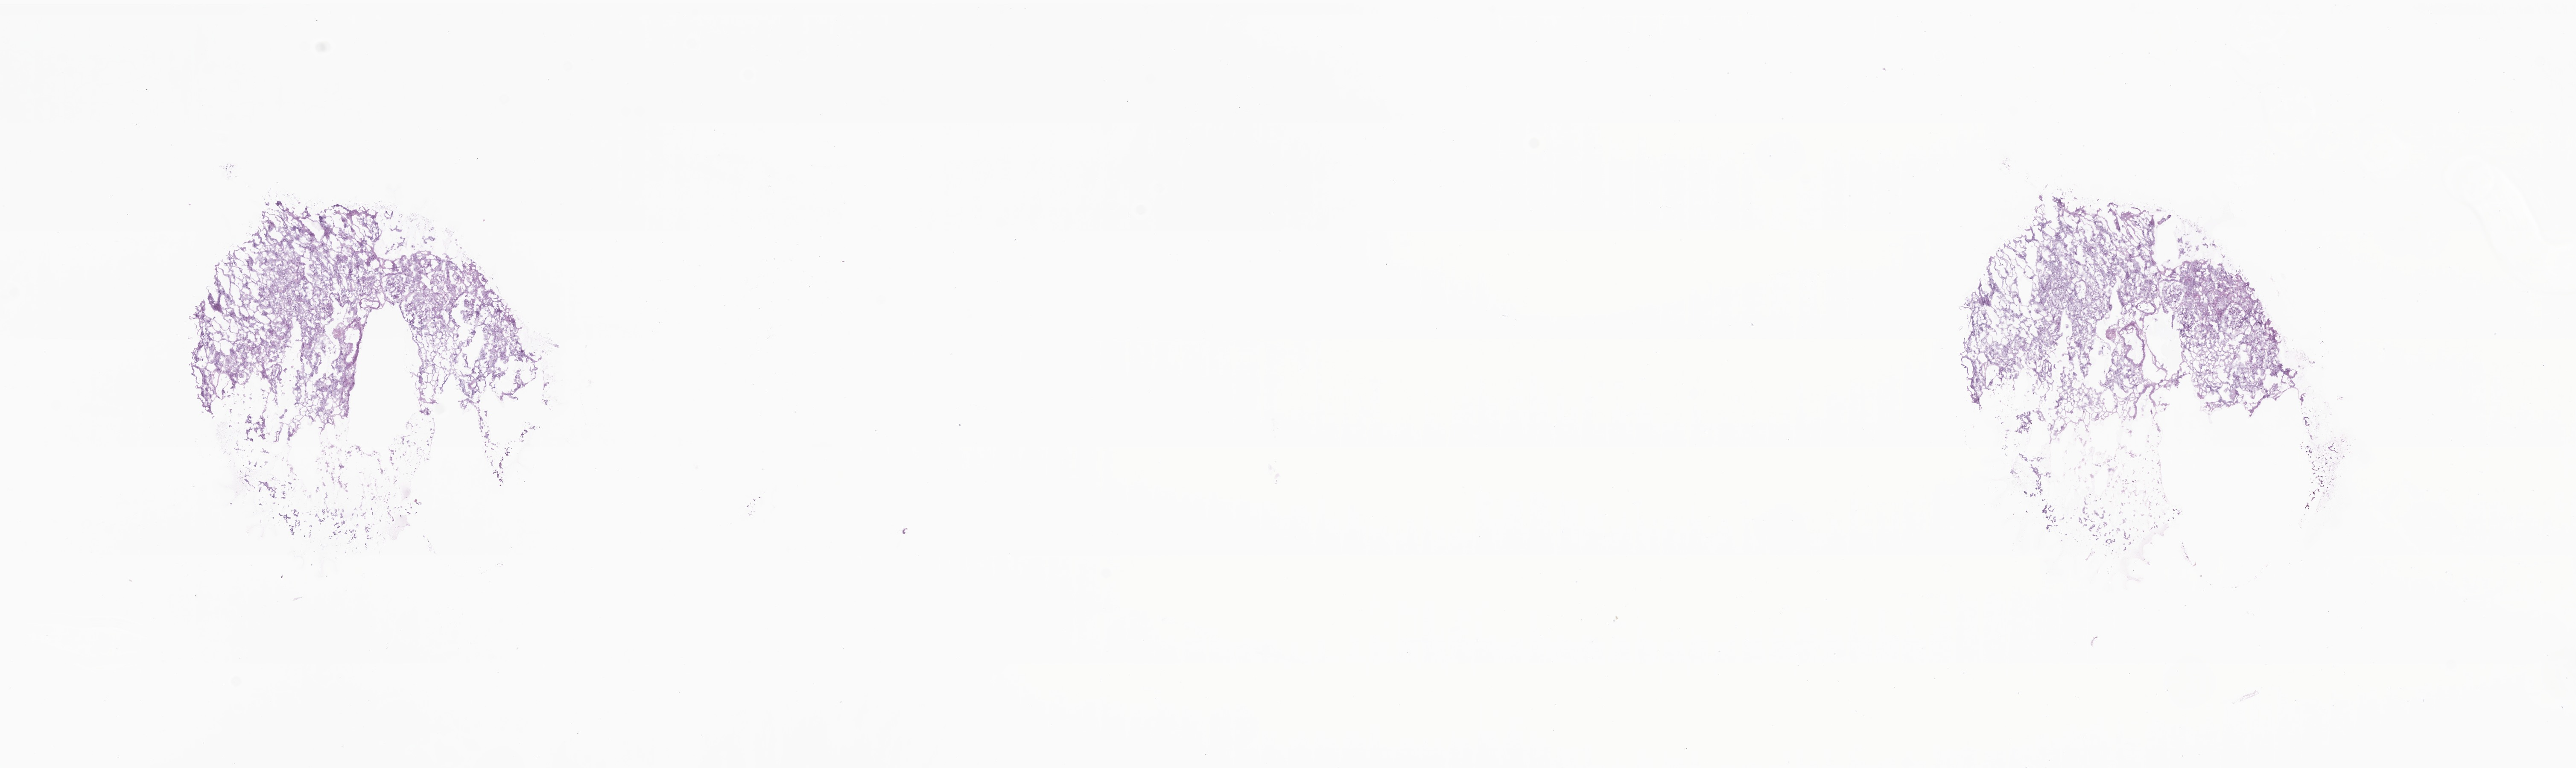
Haematoxylin and eosin whole-slide image — a low-resolution overview of the entire scanned area, about 25.4 x 7.6 mm, cryosection, specimen: normal-tissue sample (non-tumor) from a patient with clear cell adenocarcinoma, NOS, anatomic site: kidney. Patient: male, age at initial diagnosis 50 years. Pathologist review of this section (percent, as recorded): tumor cells 0%, tumor nuclei 0%, stromal cells 10%, necrosis 0%, normal cells 90%. Inflammatory infiltration, as recorded: lymphocyte infiltration 0%, monocyte infiltration 0%, neutrophil infiltration 0%.
This section: non-tumor tissue sample; the patient's diagnosis is given above.